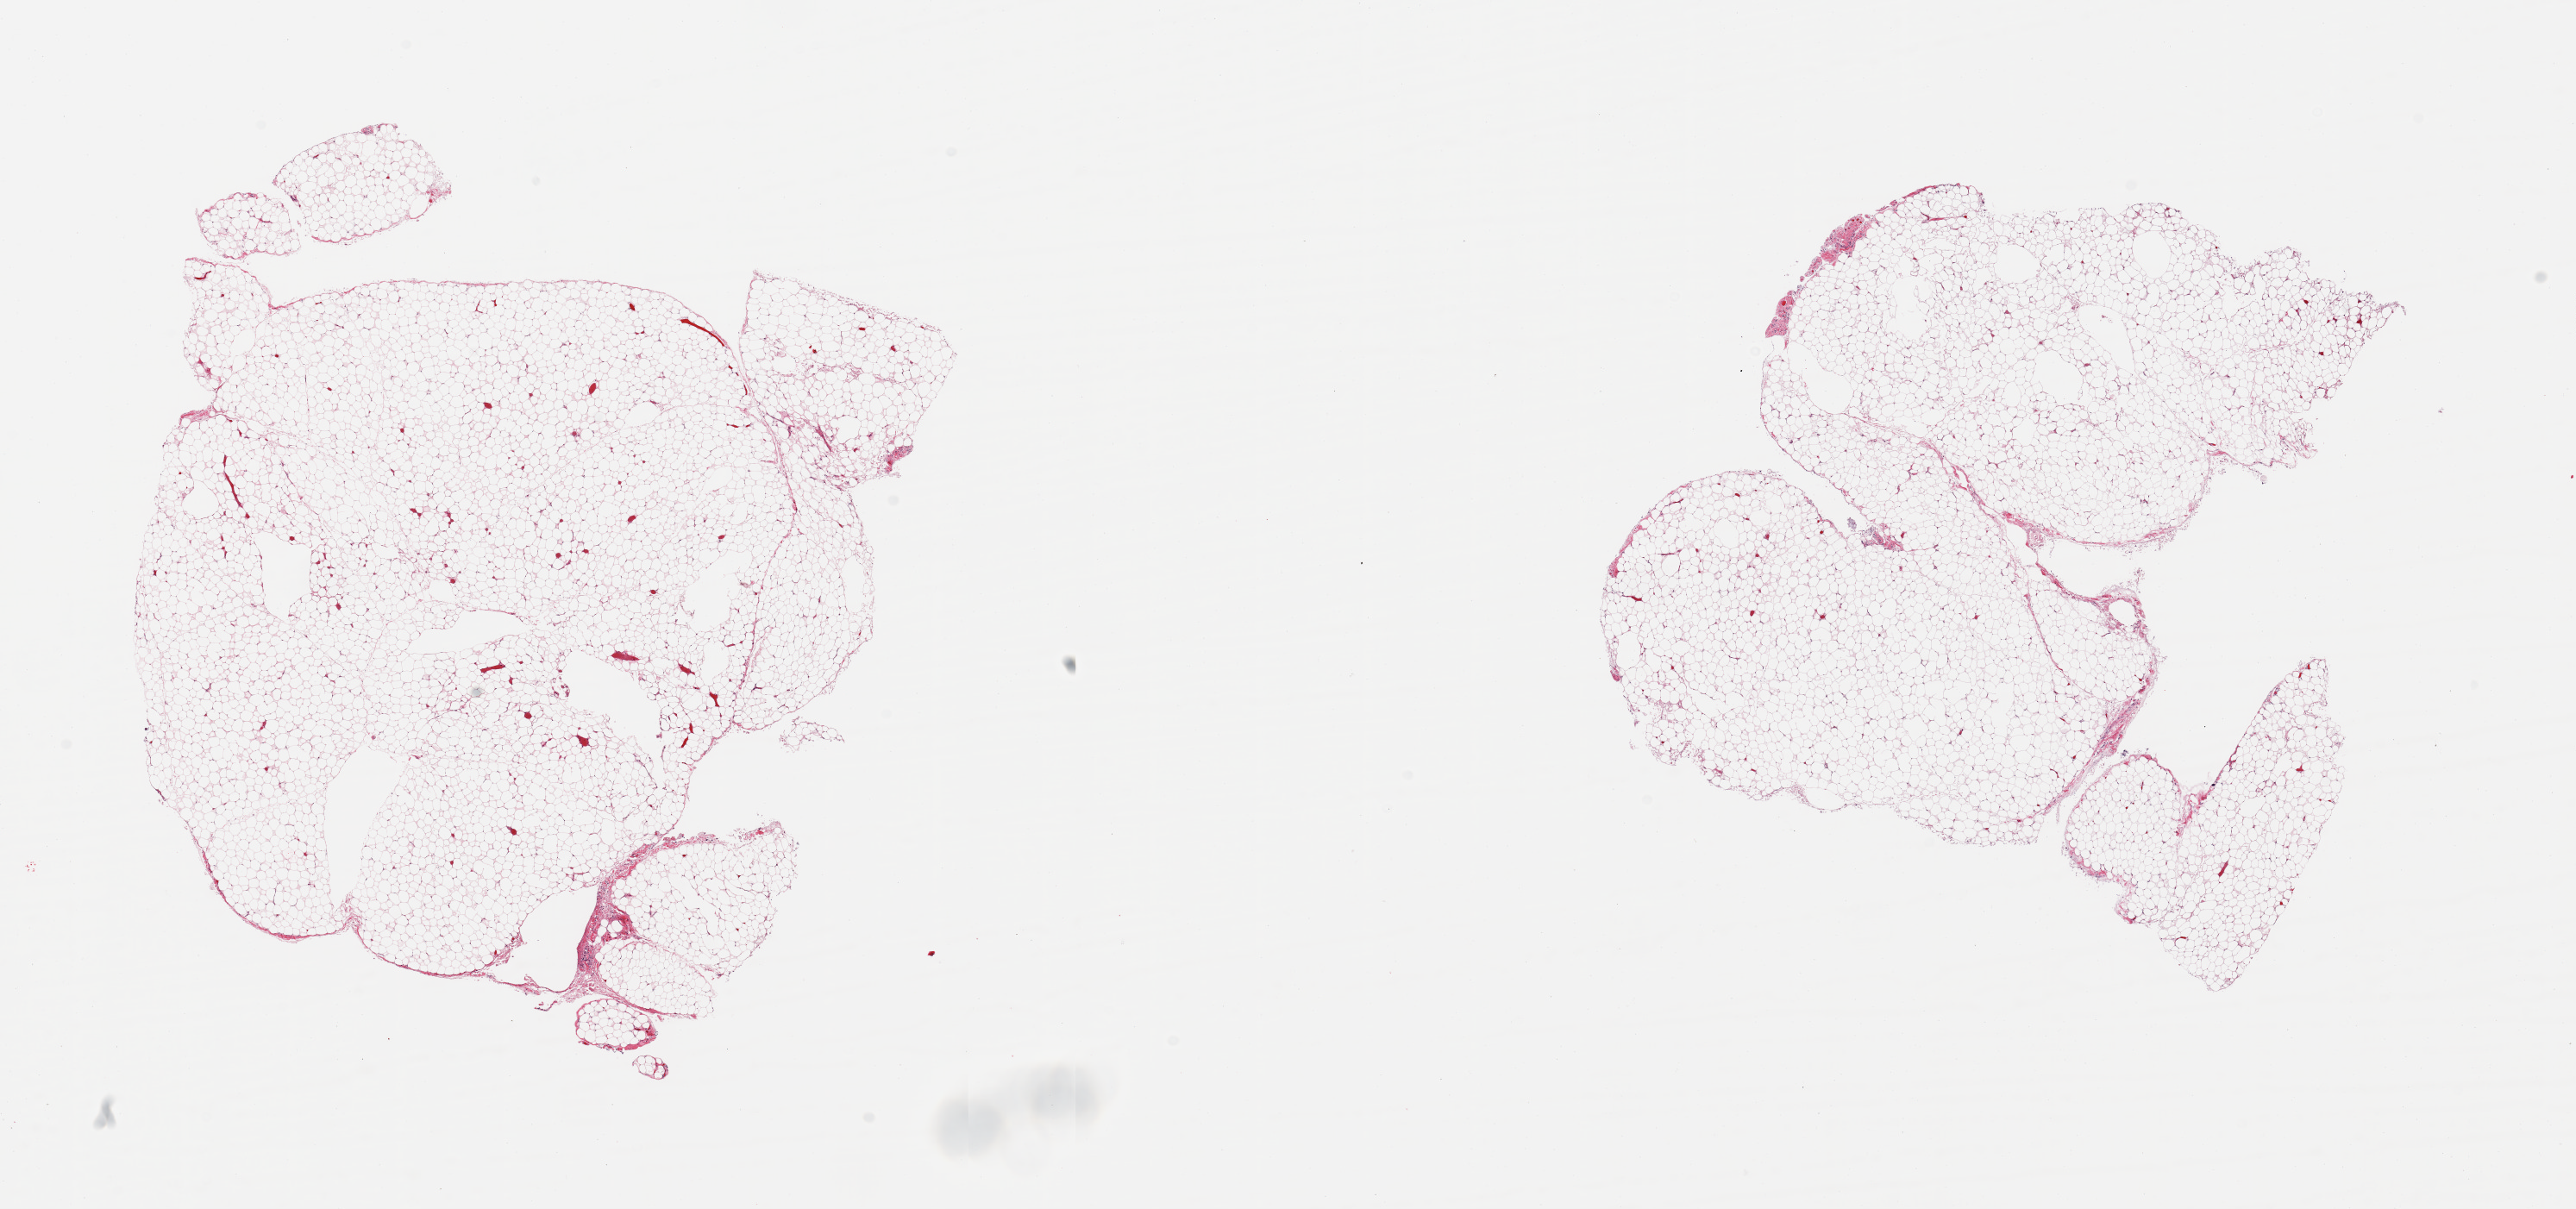
Whole-slide image, haematoxylin and eosin stain, a low-resolution overview of the entire scanned area, about 23.6 x 11.1 mm (from a 20x scan), PAXgene-fixed, paraffin-embedded tissue, target tissue: omentum, tissue donor sample. Female donor.
* review note (as recorded): 2 pieces; mature fat